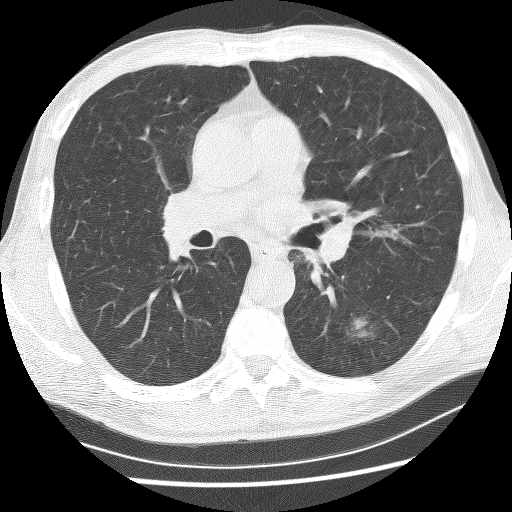
Axial slice from a low-dose chest CT screening exam, baseline annual screen, lung window (W 1500 / L -600 HU), 2.5 mm slice thickness, 120 kVp, 512 × 512 image matrix, field of view 340 × 340 mm. Male participant, aged 62 years at enrolment.
- Expert reader's lesion annotation, bounding box [x1, y1, x2, y2] px = [328, 304, 385, 350].
- Reader record for this screening exam (exam-level; its link to the box is not recorded): non-calcified nodule or mass ≥4 mm, left lower lobe, 21 × 17 mm, spiculated (stellate) margins, soft tissue attenuation.
- Later outcome: lung cancer diagnosed 58 days after this screen — non-small cell carcinoma, left lower lobe, poorly differentiated (G3), stage IA (AJCC 6th edition), 11 mm at pathology.